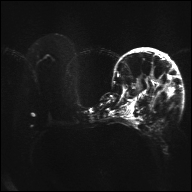
Breast MRI, one axial slice; position 19 of 32 along the scan axis; diffusion-weighted series; image 2 of 4 stored at this slice position (different b-values; order by instance number); 1.5 T; 4 mm slice thickness; 192 × 192 image matrix, field of view 360 × 360 mm. Female patient.
Structures marked on this image (manually delineated by an expert):
- tumour on diffusion-weighted imaging: bounding box (x1, y1, x2, y2) in pixels: (152, 77, 159, 83)